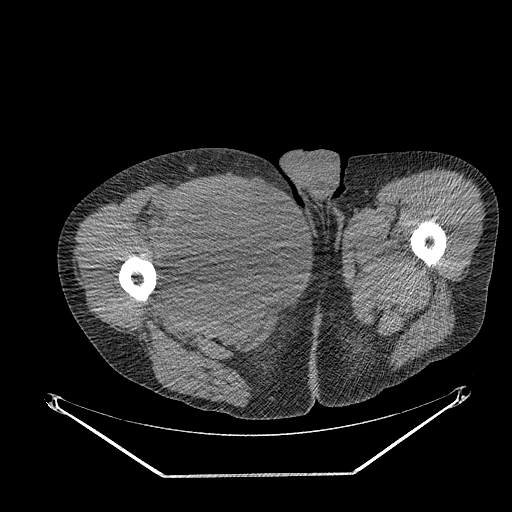
CT of an extremity soft-tissue mass (from a PET/CT study), one axial slice; position 276 of 311 along the scan axis; reconstruction kernel STANDARD; 140 kVp; soft-tissue window (W 400 / L 40 HU); 3.75 mm slice thickness; 512 × 512 image matrix. Male patient. Case-level facts recorded for this patient, not image findings: histological type: undifferentiated - pleiomorphic; grade: high; site of the primary tumour: right thigh.
Outlined on this slice (expert contour drawn on MRI and transferred to this co-registered scan by the dataset authors):
- gross tumour volume including surrounding oedema: bounding box <165,180,264,280> (left, top, right, bottom; pixels)
- gross tumour volume (mass): <165,180,264,280>